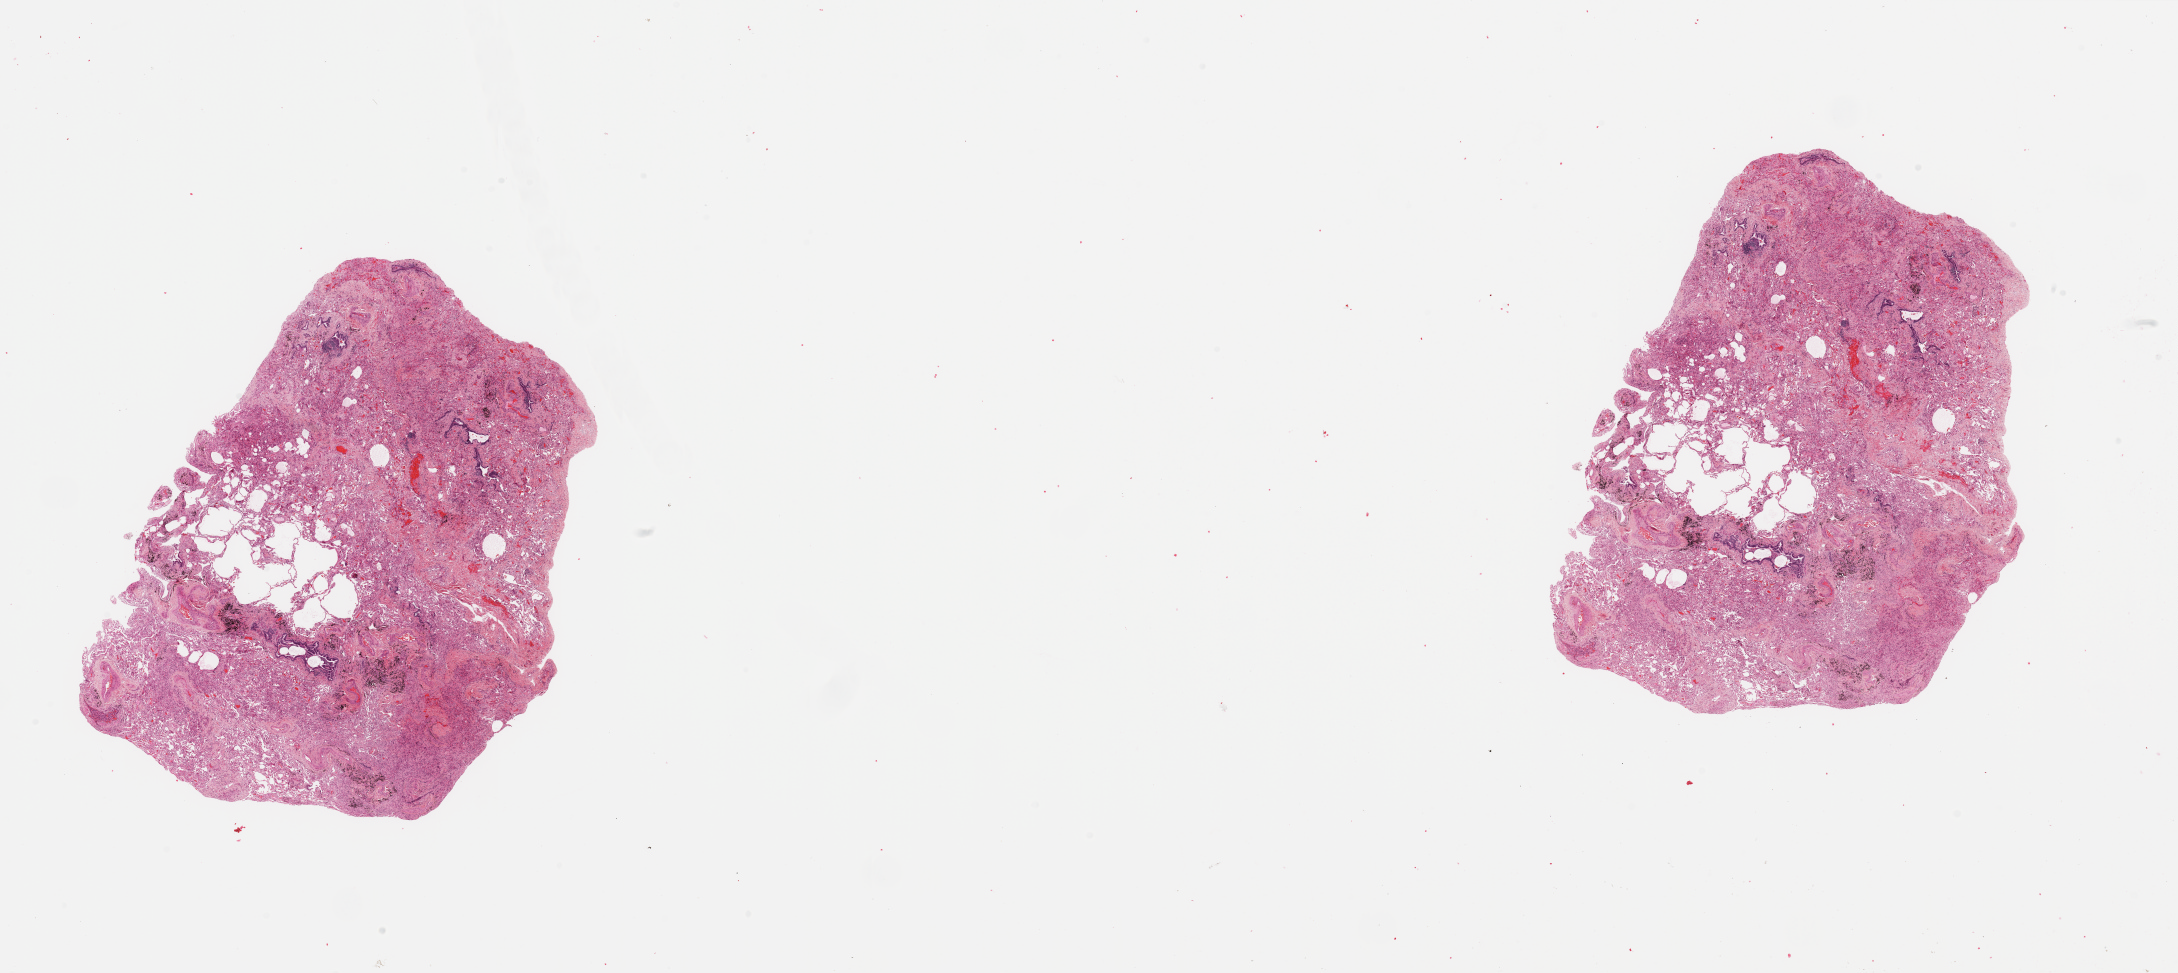
Whole-slide histology image, H&E — a low-resolution overview of the entire scanned area, about 34.5 x 15.4 mm; lung, tumour tissue. 69-year-old female patient.
Histologic diagnosis: Adenocarcinoma, NOS.